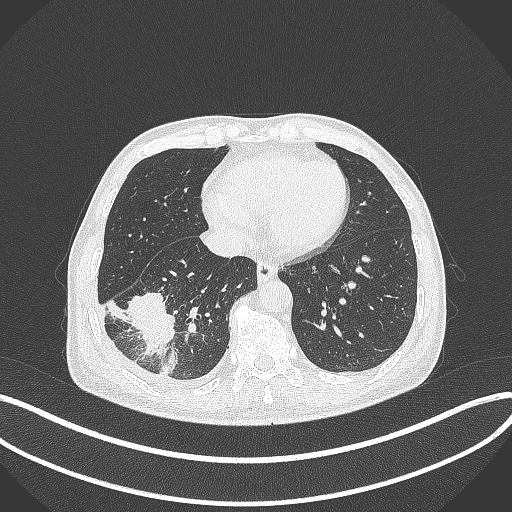
Chest CT, one axial slice; slice 117 of 388 in the series (ordered by position); 120 kVp; lung window (W 1500 / L -600 HU); 1 mm slice thickness; 512 × 512 image matrix. Male patient, age 64 years. Case-level facts recorded for this patient, not image findings: clinical TNM (as recorded): T3 N0 M0; histopathological grade: G2-3.
Annotated regions visible in this slice (bounding box drawn by a radiologist):
- lung tumour (recorded histology: adenocarcinoma): bounding box <125,285,179,357> (left, top, right, bottom; pixels)